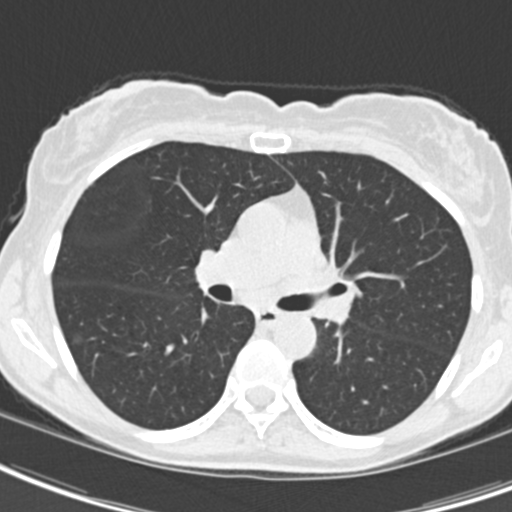
Axial slice from a low-dose chest CT screening exam. Baseline screening round. Lung window (W 1500 / L -600 HU). Standard (soft-tissue) reconstruction kernel (B30f). Slice 70 of 189 in the series. Female, age 62 years at enrolment. Current smoker at enrolment.
- Lesion marked by an expert reader, bounding box <297,243,375,327> (left, top, right, bottom; pixels).
- Screening reader's record for this exam (one nodule recorded; not confirmed to be the boxed lesion): non-calcified nodule or mass ≥4 mm, right upper lobe, 24 × 20 mm, smooth margins, ground glass attenuation.
- Note: the box lies in the patient's left hemithorax on this image, whereas the reader's record names the right lung; they may be different findings.
- Participant outcome: lung cancer diagnosed 24 days after this screen — oat cell carcinoma, left hilum, left main stem bronchus, stage IIIB (AJCC 6th edition), 50 mm at pathology.